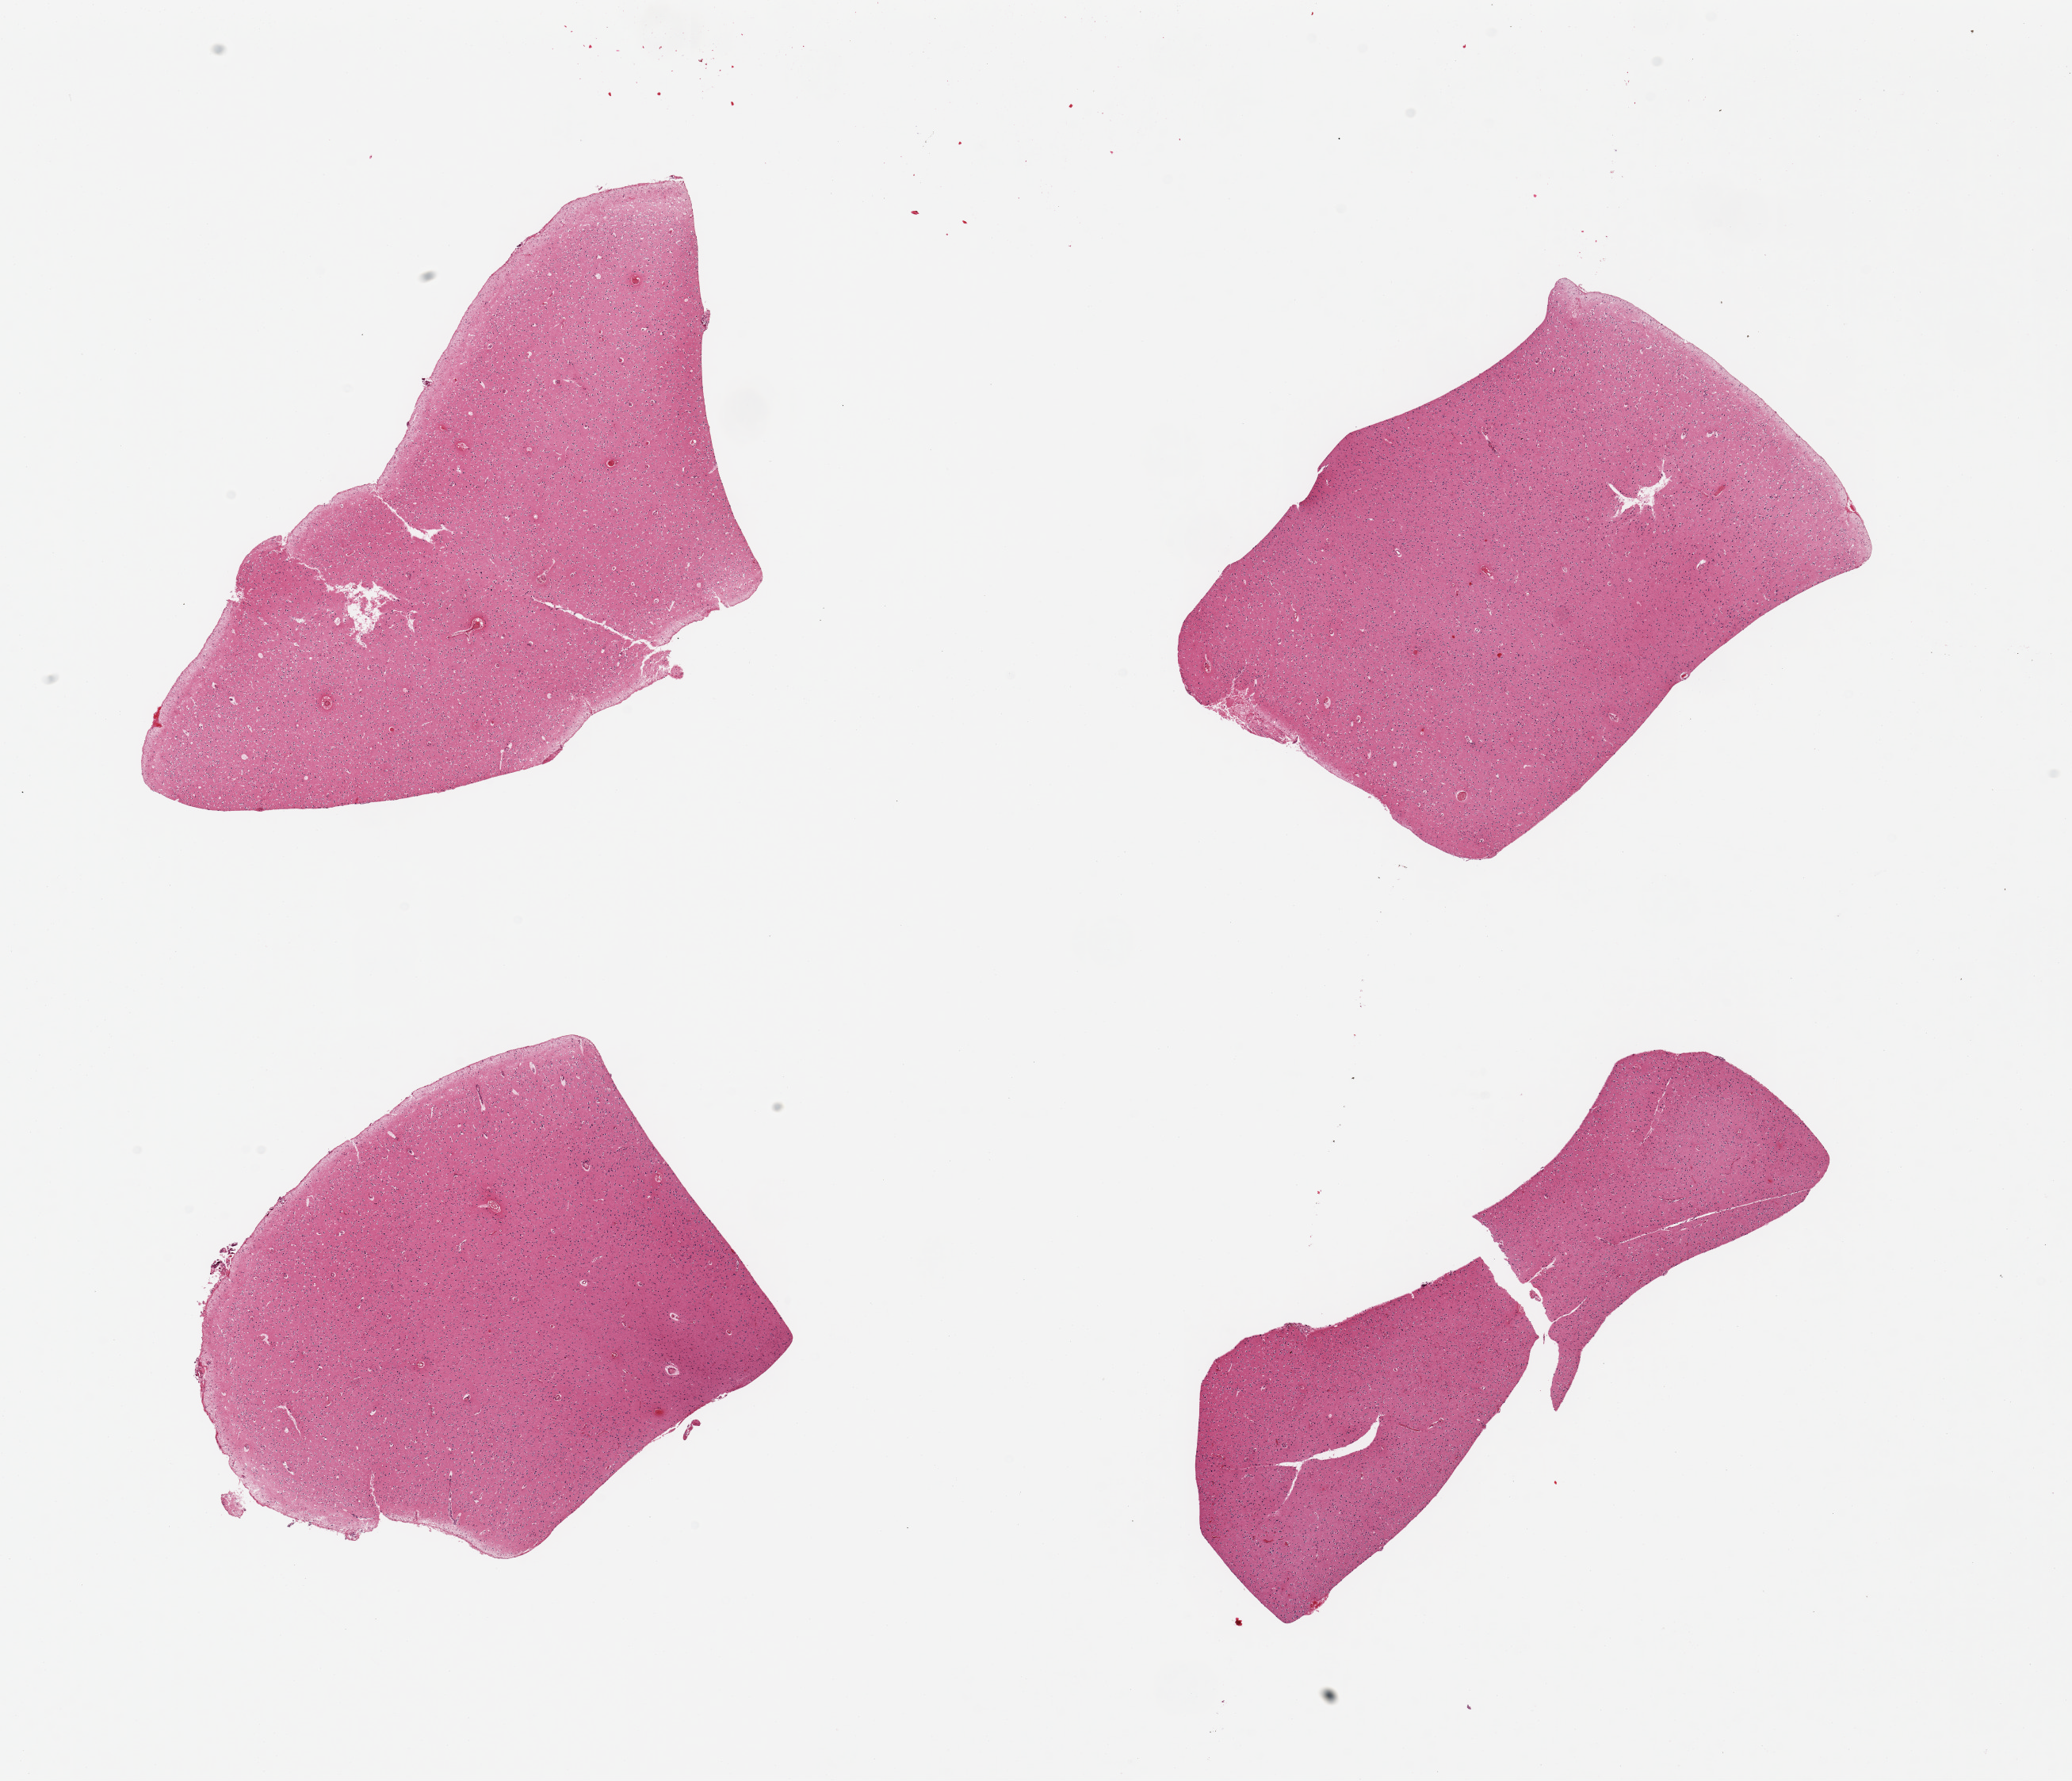
Digitized H&E-stained section, shown as a low-resolution overview of the whole scanned area (about 20.7 x 17.8 mm), PAXgene-fixed paraffin-embedded (PFPE) section, sampled site (target tissue): cerebral cortex, donor tissue sample. Male donor.
• review note (as recorded): 4 pieces, no abnormalities